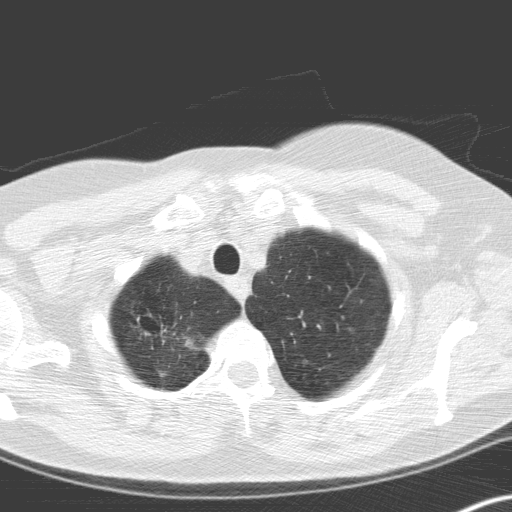
Low-dose screening chest CT, axial slice, second screening round (one year after baseline), lung window (W 1500 / L -600 HU), 3.2 mm slice thickness, standard (soft-tissue) reconstruction kernel (C), 512 × 512 image matrix. Female, age 60 years at enrolment.
Lesion marked by an expert reader, box from (x=128, y=305) to (x=211, y=380) px. The exam's reader record, not a measurement of the box and not confirmed to be the same lesion: non-calcified nodule or mass ≥4 mm, right upper lobe, 12 × 8 mm, spiculated (stellate) margins, soft tissue attenuation, pre-existing on the prior screen: no. Later outcome: lung cancer diagnosed 58 days after this screen — squamous cell carcinoma, keratinizing, NOS, right upper lobe, moderately differentiated (G2), stage IA (AJCC 6th edition), 20 mm at pathology.